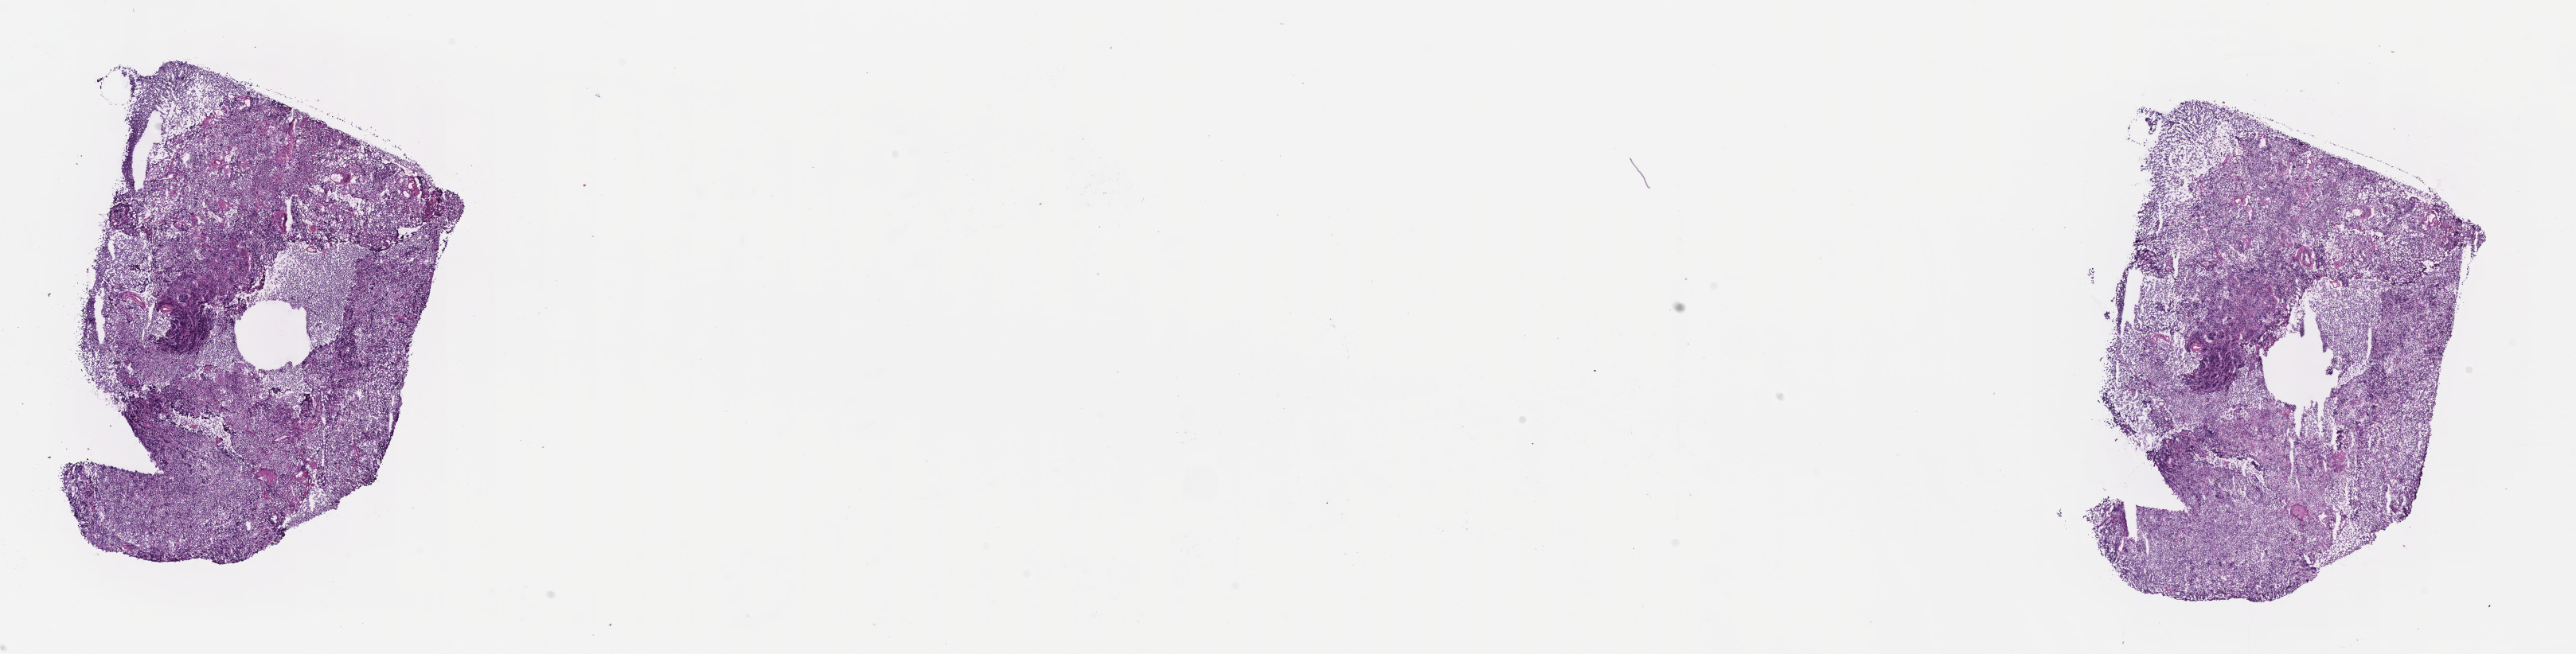
Whole-slide image, H&E stain, low-resolution overview of the scanned area, about 26.2 x 6.6 mm; frozen section (tissue freezing medium); primary tumor; anatomic site: lymph node of head and neck. Female patient; age at initial diagnosis 8 years. Composition of this section per pathologist review: tumor cells 85%, tumor nuclei 85%, stromal cells 15%, necrosis 0%, normal cells 0%. Inflammatory infiltration, as recorded: lymphocyte infiltration 20%, monocyte infiltration 30%, neutrophil infiltration 10%.
Diagnosis: Burkitt lymphoma, NOS.